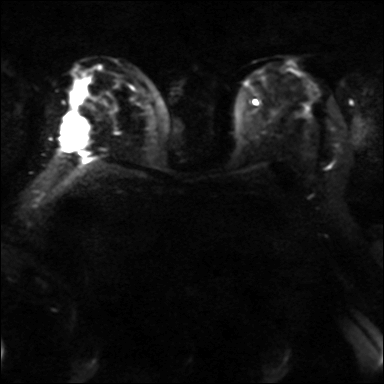
Breast MRI, one axial slice; slice 20 of 42 in the series (ordered by position); diffusion-weighted series; image 2 of 4 stored at this slice position (different b-values; order by instance number); 3 T; 384 × 384 image matrix, field of view 320 × 320 mm. Female patient.
Structures marked on this image (manually delineated by an expert):
- tumour on diffusion-weighted imaging: bounding box [x1, y1, x2, y2] px = [61, 117, 89, 151]